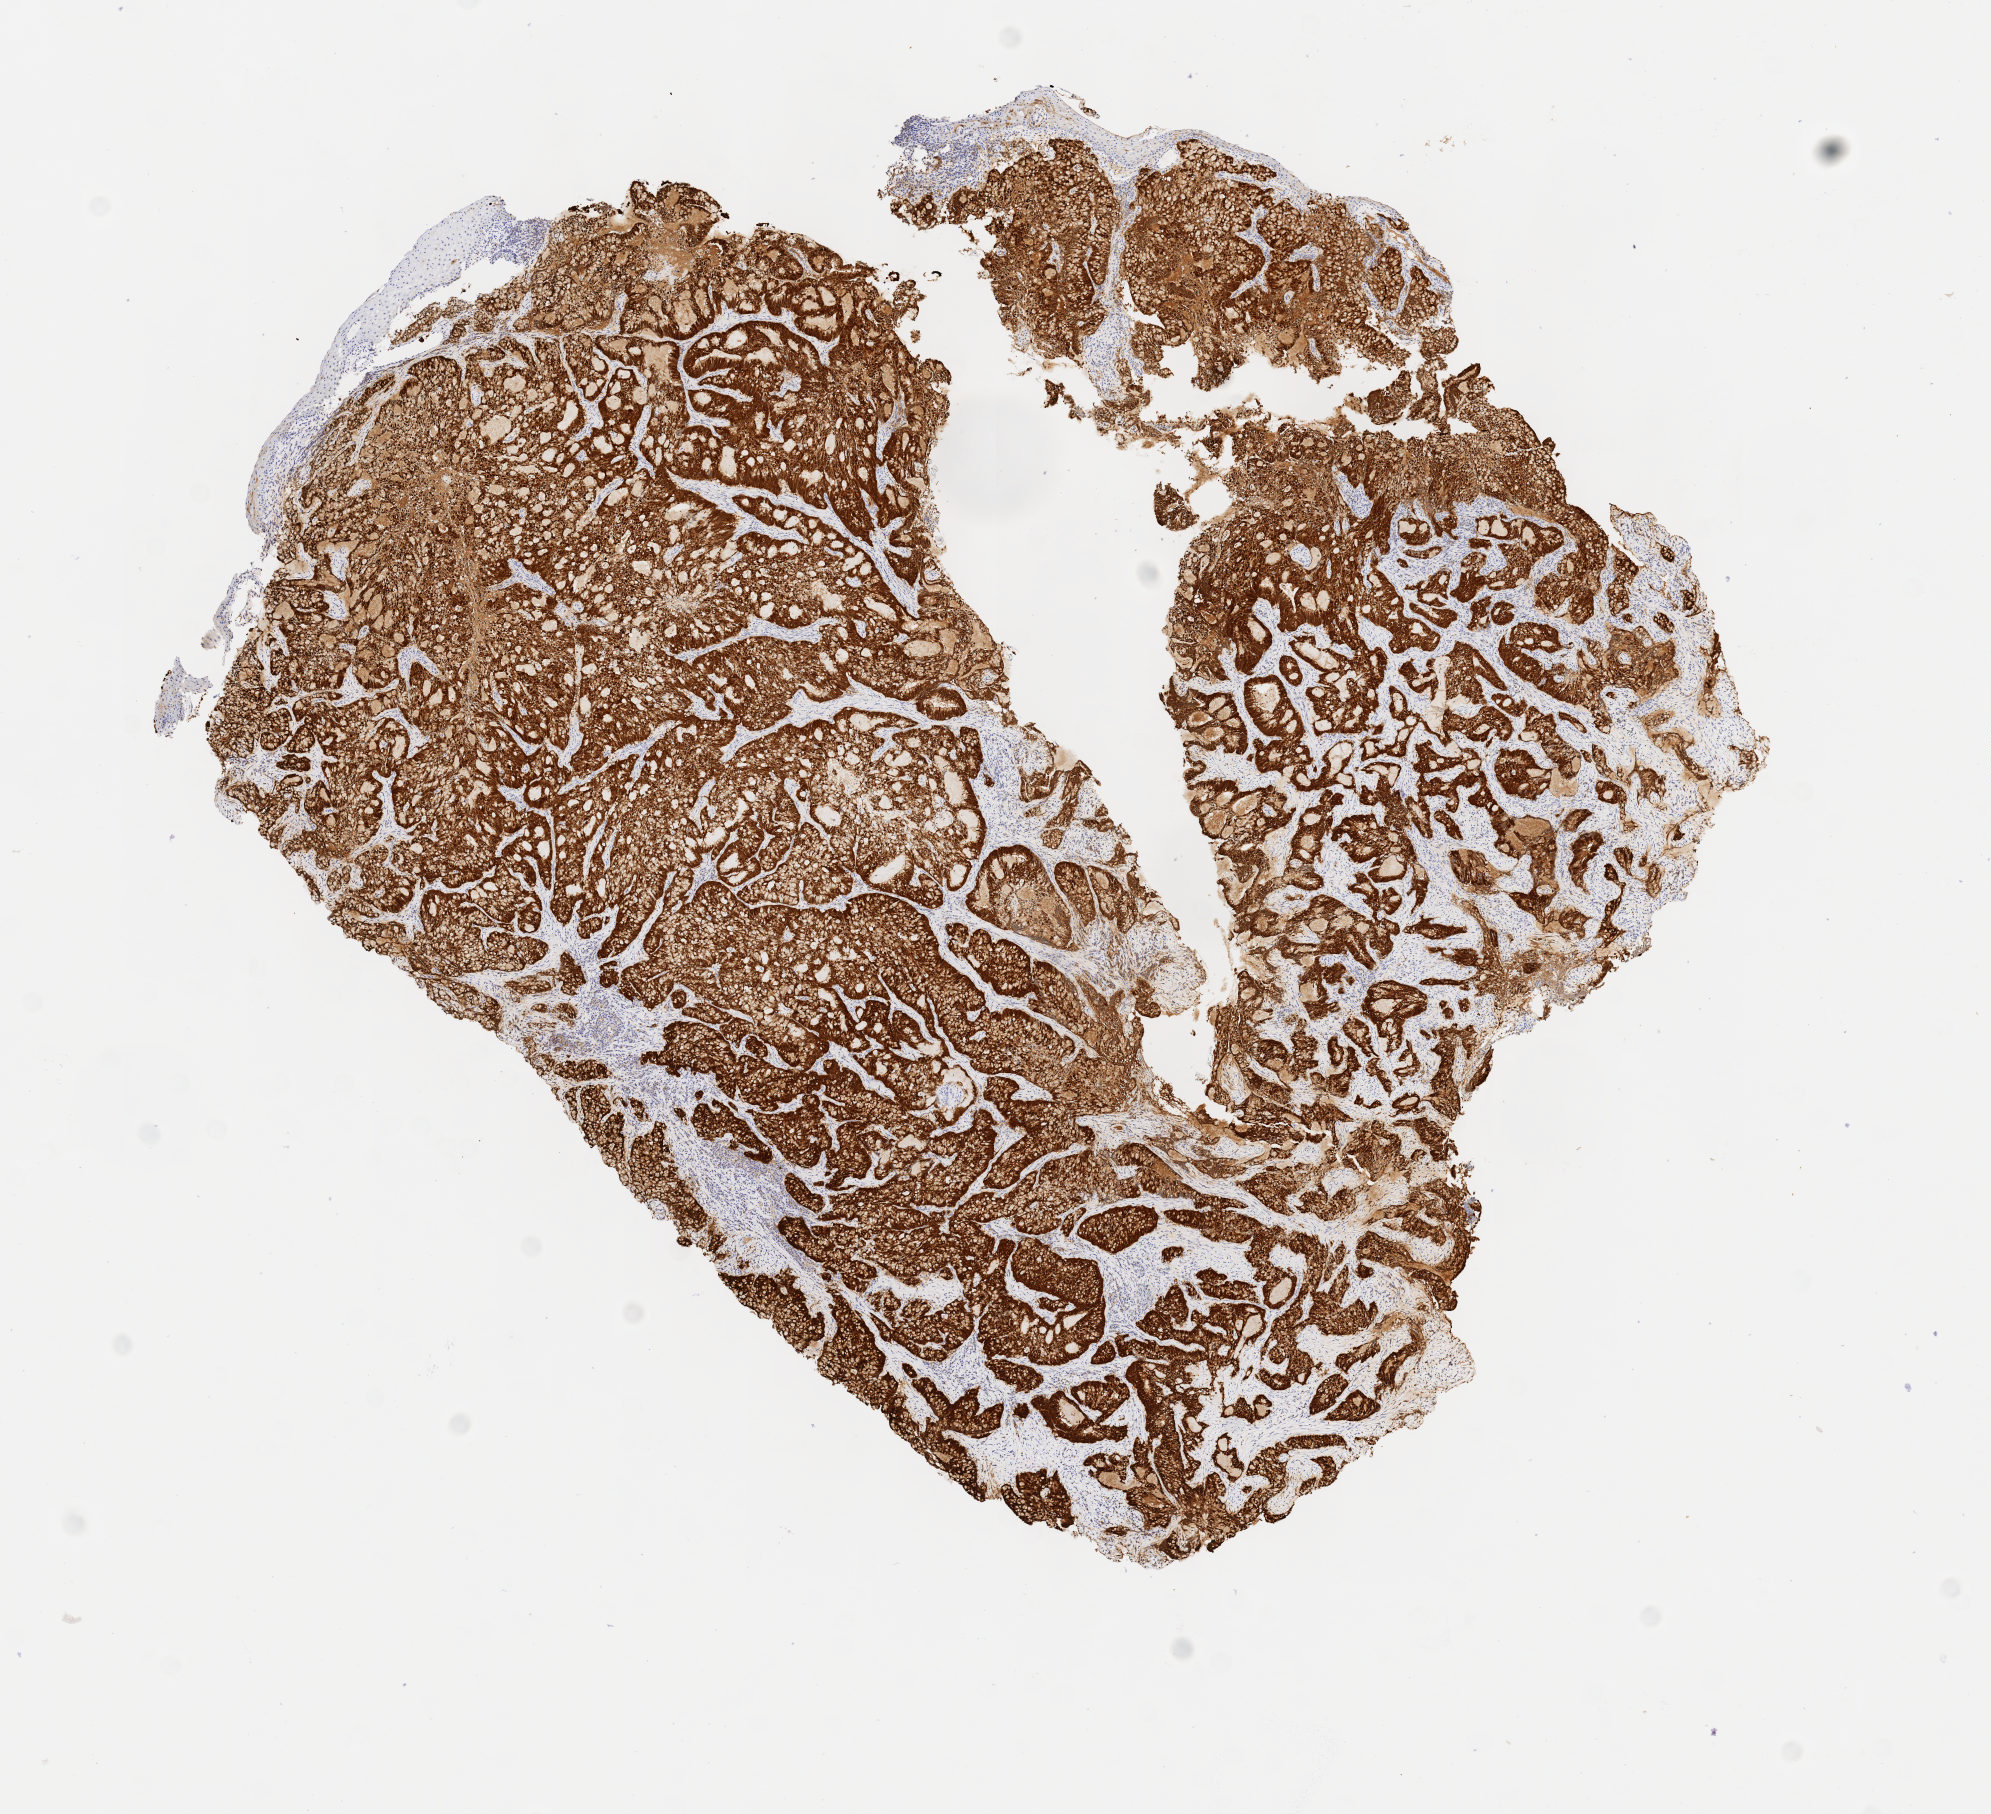
Whole-slide image, immunohistochemical stain for p16 (p16INK4a), whole scanned area (about 8.1 x 7.3 mm) shown as a low-resolution overview. Specimen: tumor tissue. Anatomic site: cervix. Patient female; 28 years old.
- diagnosis: Adenocarcinoma, NOS